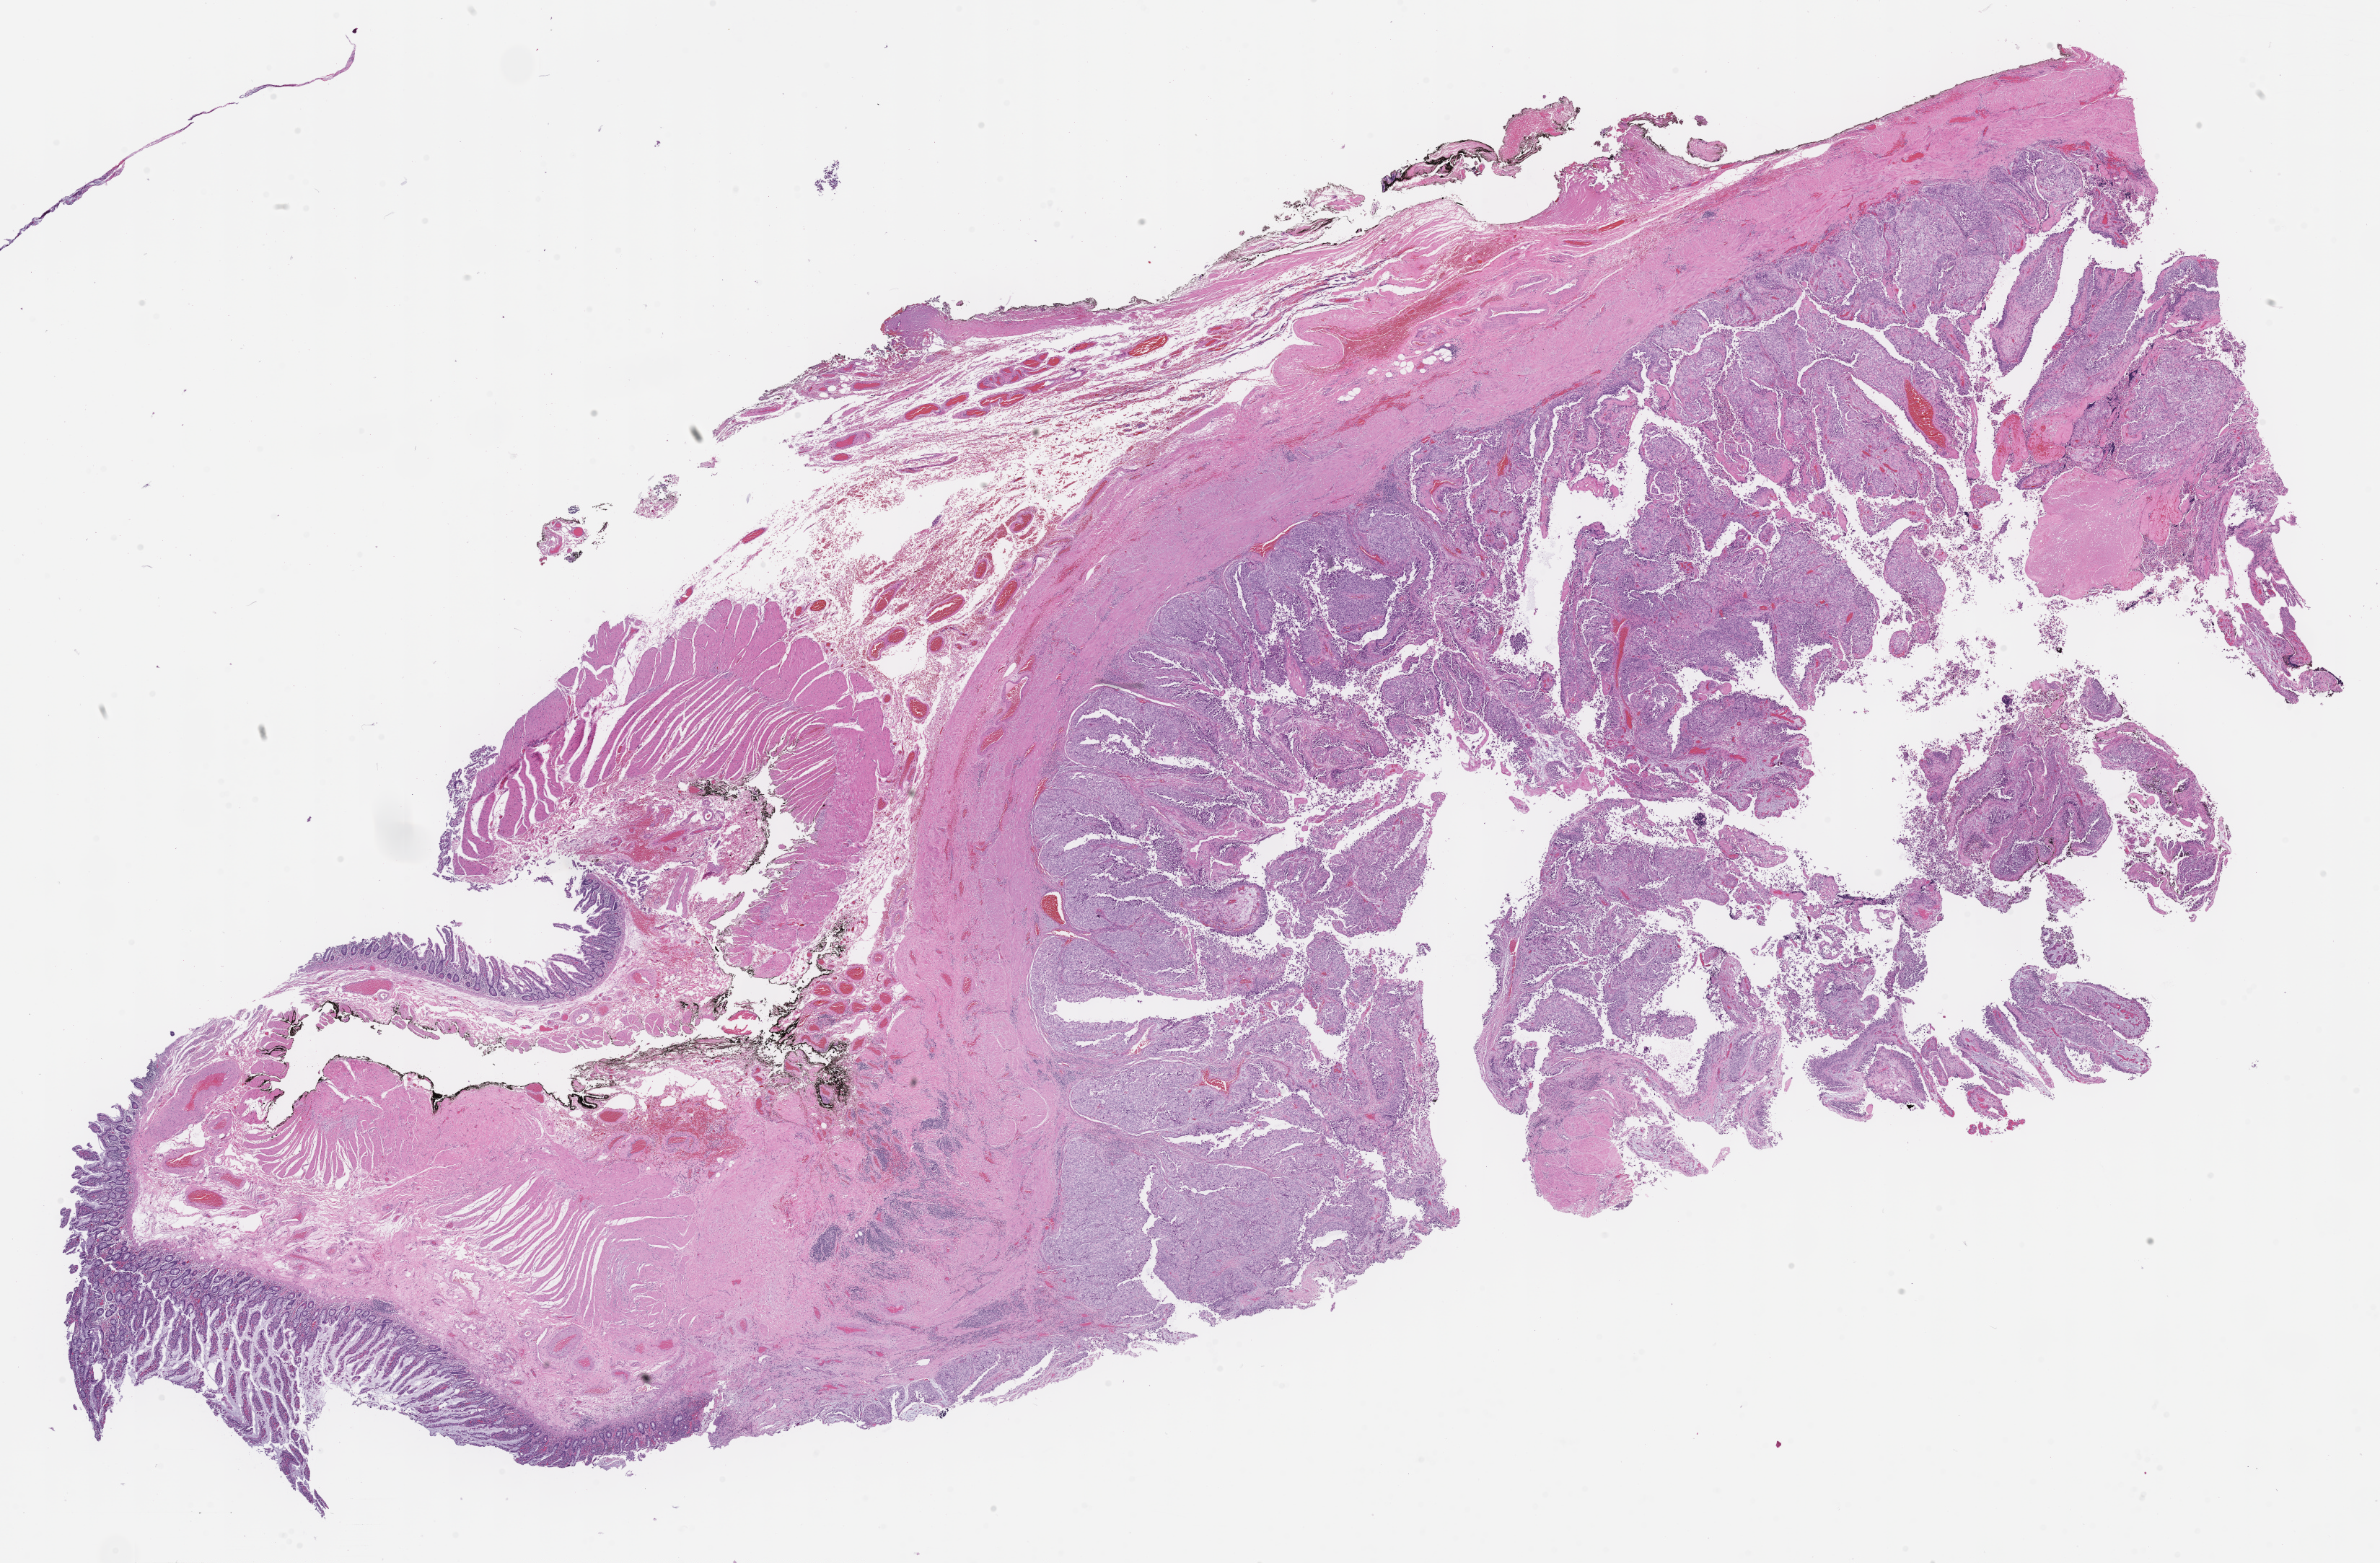
H&E whole-slide image, low-resolution overview of the scanned area, about 26.6 x 17.5 mm, formalin-fixed paraffin-embedded section, specimen: recurrent tumor. Male patient.
Patient diagnosis: Carcinoma, metastatic, NOS.